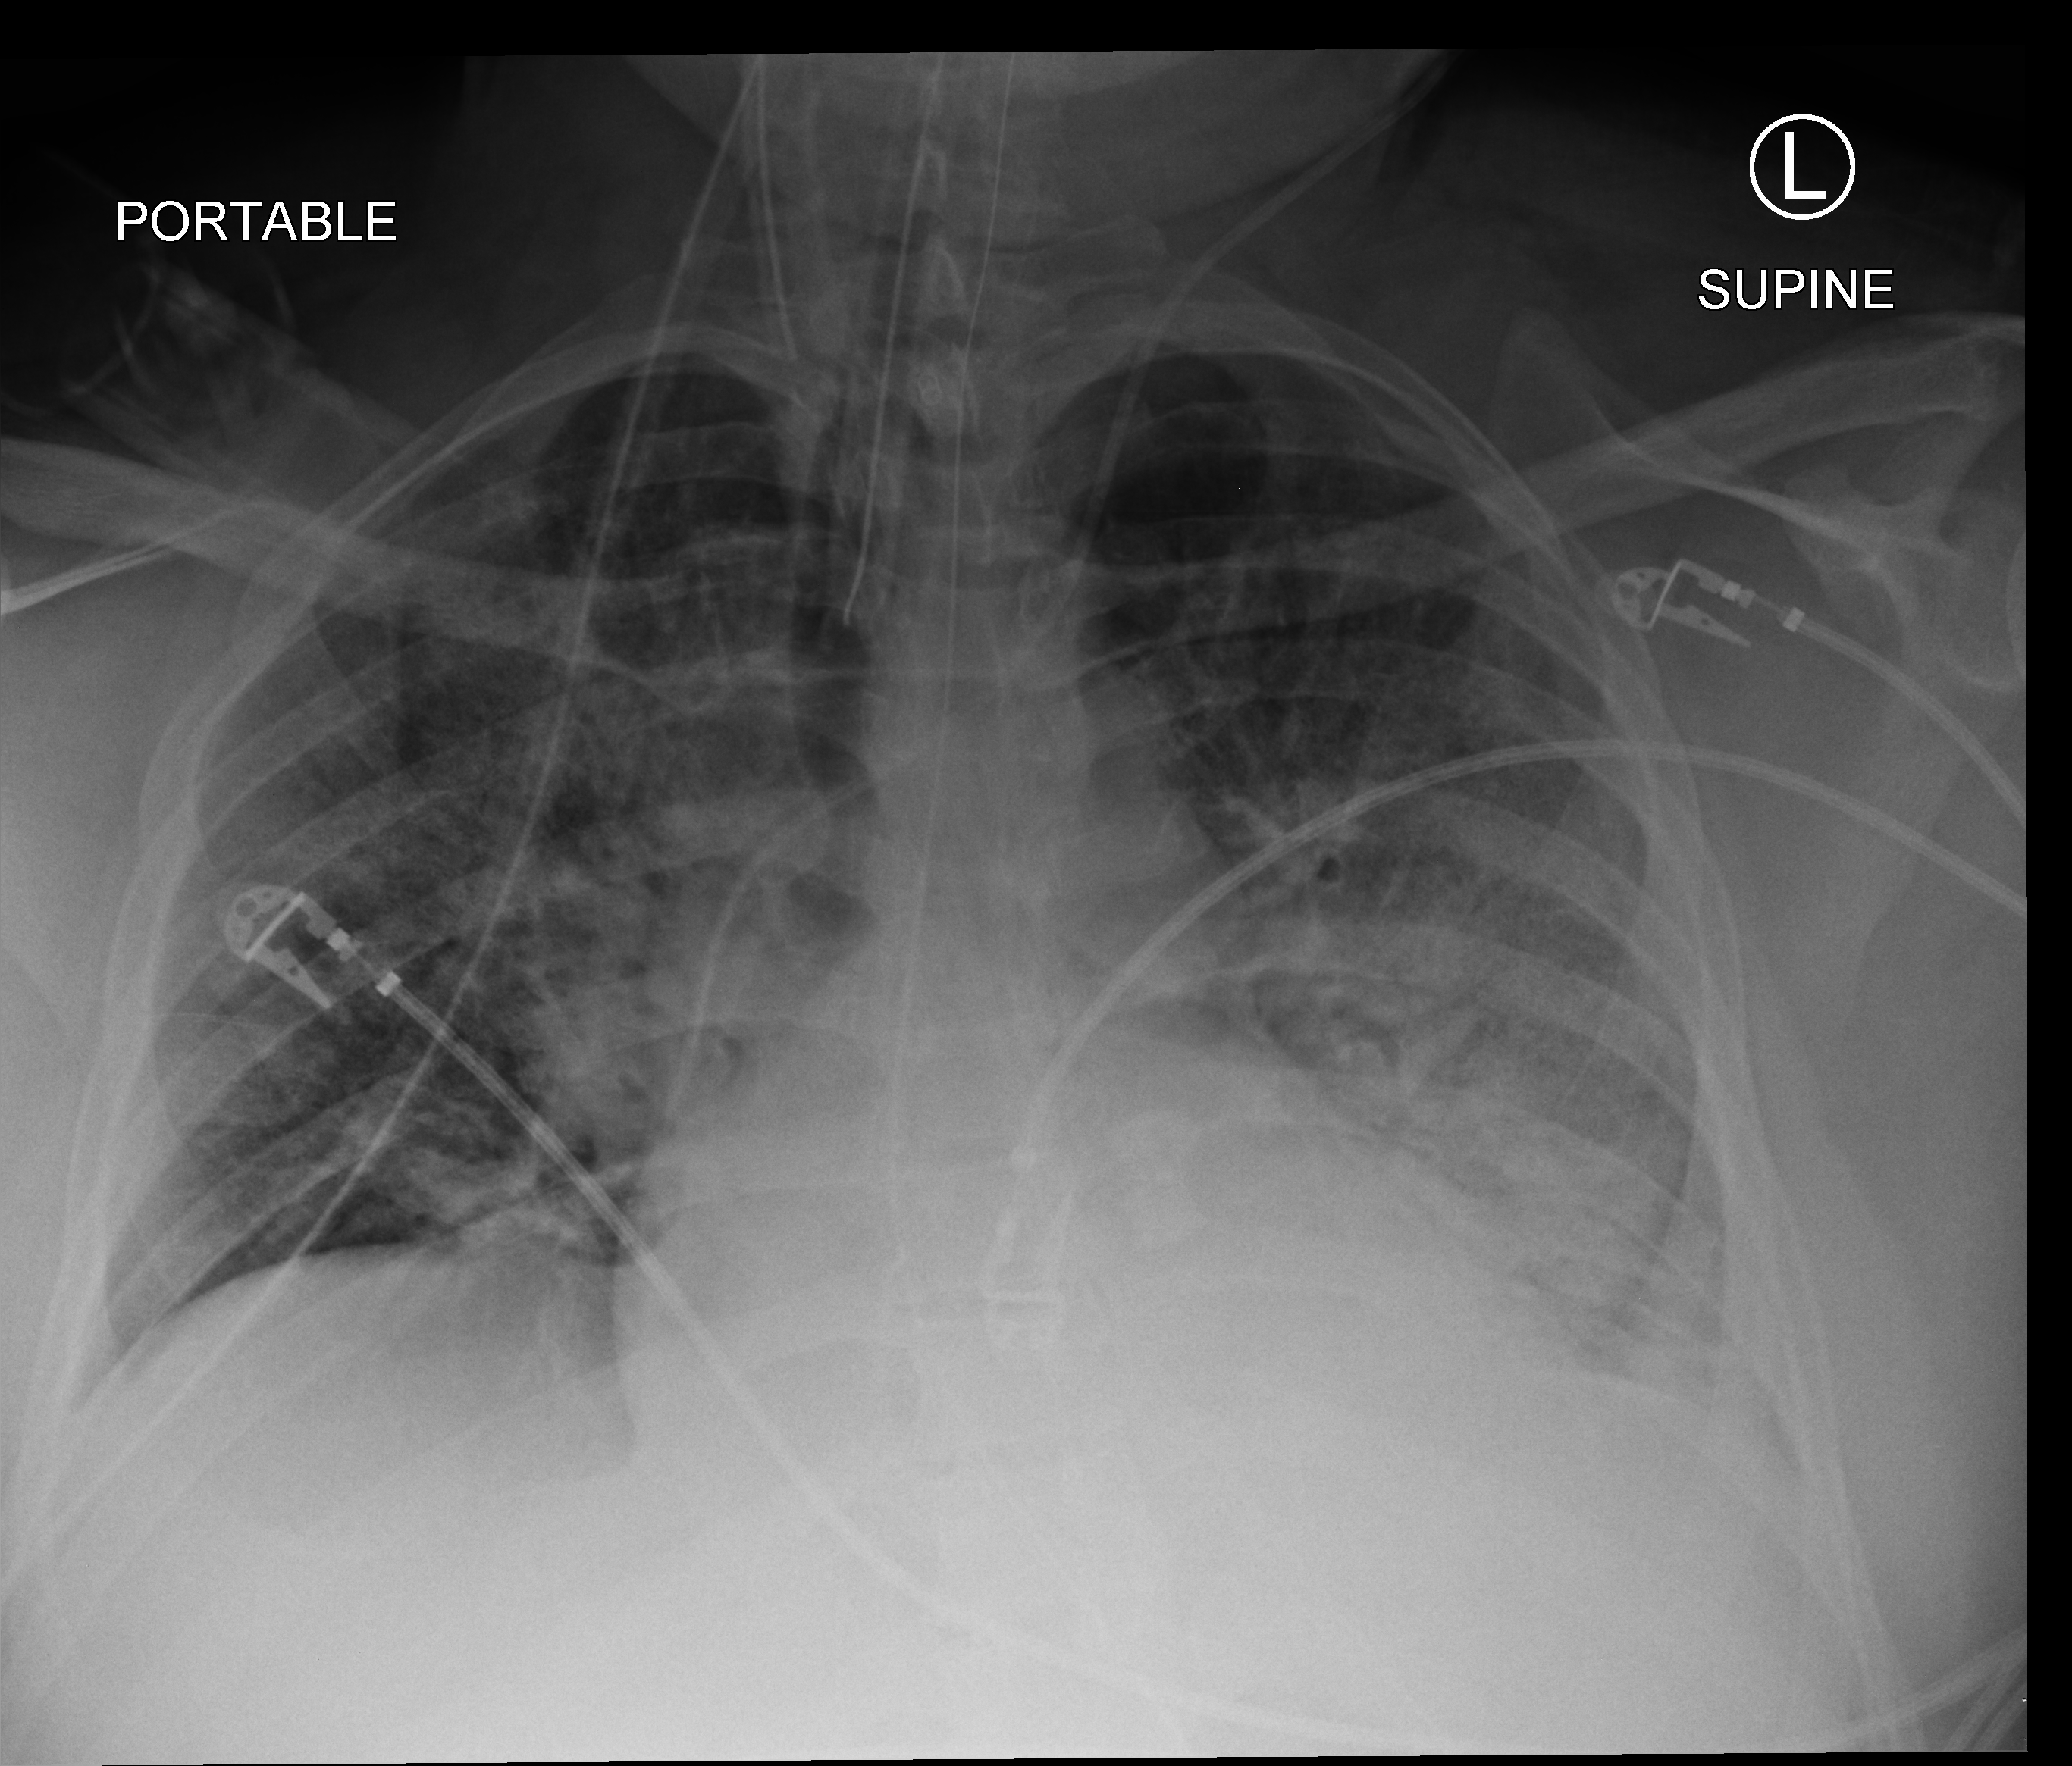
Bedside chest radiograph (computed radiography). Adult patient hospitalised with COVID-19, age 18–59 years.
From the hospital-stay record, not from the radiograph (when in the stay this image was taken is not recorded): other chronic lung disease (admission record): yes; smoking status (admission record): never; mechanically ventilated during this hospital stay: yes.